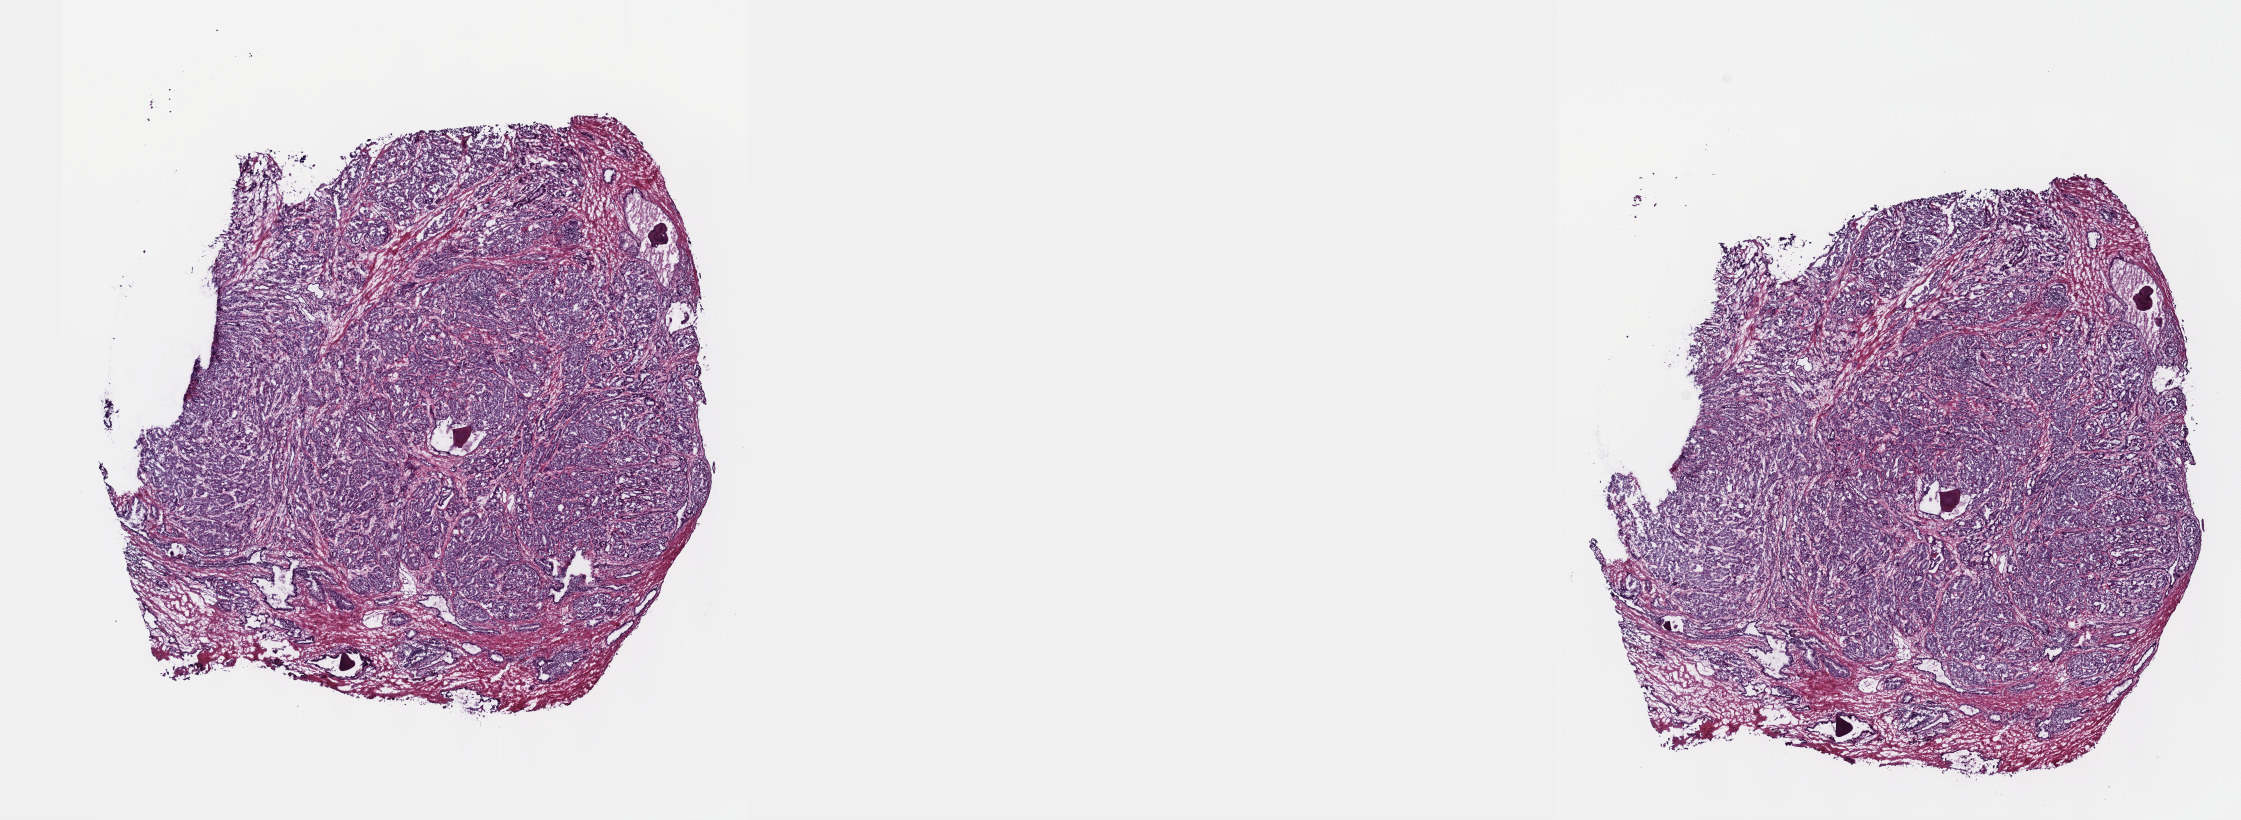
Digitized H&E-stained tissue section (whole slide) — shown as a low-resolution overview of the whole scanned area (about 18.1 x 6.6 mm, slide scanned at 40x), frozen section from the top of the tissue portion, prostate, primary tumour sample. Male, age 72 years at initial diagnosis. Gleason score: 8 (4+4). Slide review estimates, as recorded: tumour cells 85%, tumour nuclei 90%, normal cells 0%, stromal cells 15%, necrosis 0%. Infiltration values recorded for this section: lymphocyte infiltration 0%, monocyte infiltration 0%, neutrophil infiltration 0%.
Pathologic diagnosis: Adenocarcinoma, NOS (prostate gland). Laterality: bilateral. Lymph nodes positive (case pathology): 0 of 4 examined.